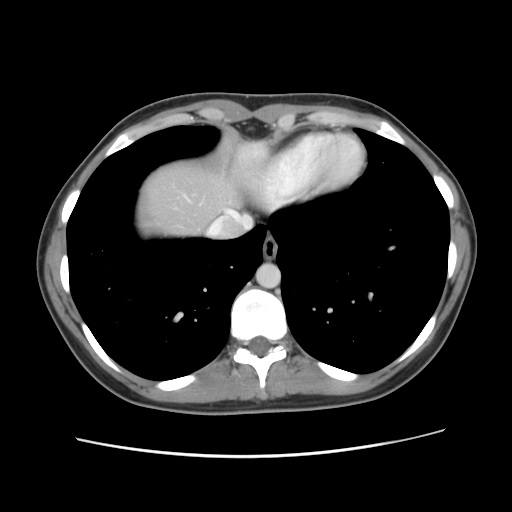
Contrast-enhanced abdominal CT, one axial slice. Position 115 of 134 along the scan axis. Intravenous contrast given. Soft-tissue window (W 400 / L 40 HU). 2.5 mm slice thickness. 512 × 512 image matrix, field of view 339 × 339 mm. Female patient, age 33 years. Case-level facts recorded for this patient, not image findings: diagnosis: colorectal cancer liver metastases, imaged before liver resection; multiple liver metastases: yes; largest metastasis: 4.5 cm; chemotherapy before resection: no.
Structures marked on this image (manually delineated by an expert):
- hepatic veins: bounding box (x1, y1, x2, y2) in pixels: (229, 211, 232, 213)
- liver: (134, 157, 243, 240)
- planned liver remnant (the part of the liver to remain after resection): (134, 157, 243, 240)